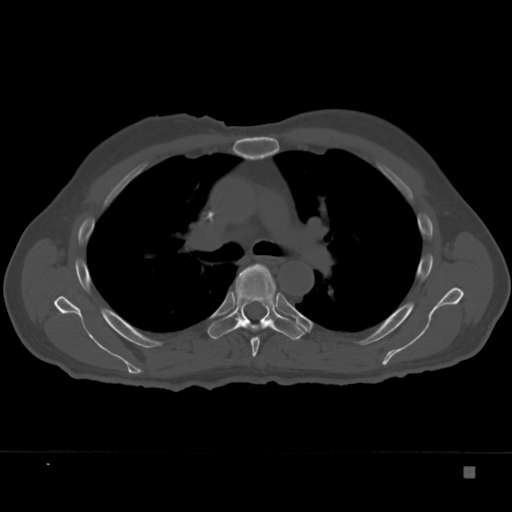
CT including the spine, one axial slice. Position 246 of 332 along the scan axis. Reconstruction kernel Br40s. 120 kVp. Bone window (W 1800 / L 400 HU). 1.5 mm slice thickness. 512 × 512 image matrix. Male patient, age 72 years. Case-level facts recorded for this patient, not image findings: primary cancer: skeletal.
Outlined on this slice (semi-automatic segmentation, software-assisted and operator-edited):
- T5 vertebra: bounding box (x1, y1, x2, y2) in pixels: (251, 296, 277, 357)
- T6 vertebra: (207, 263, 305, 341)